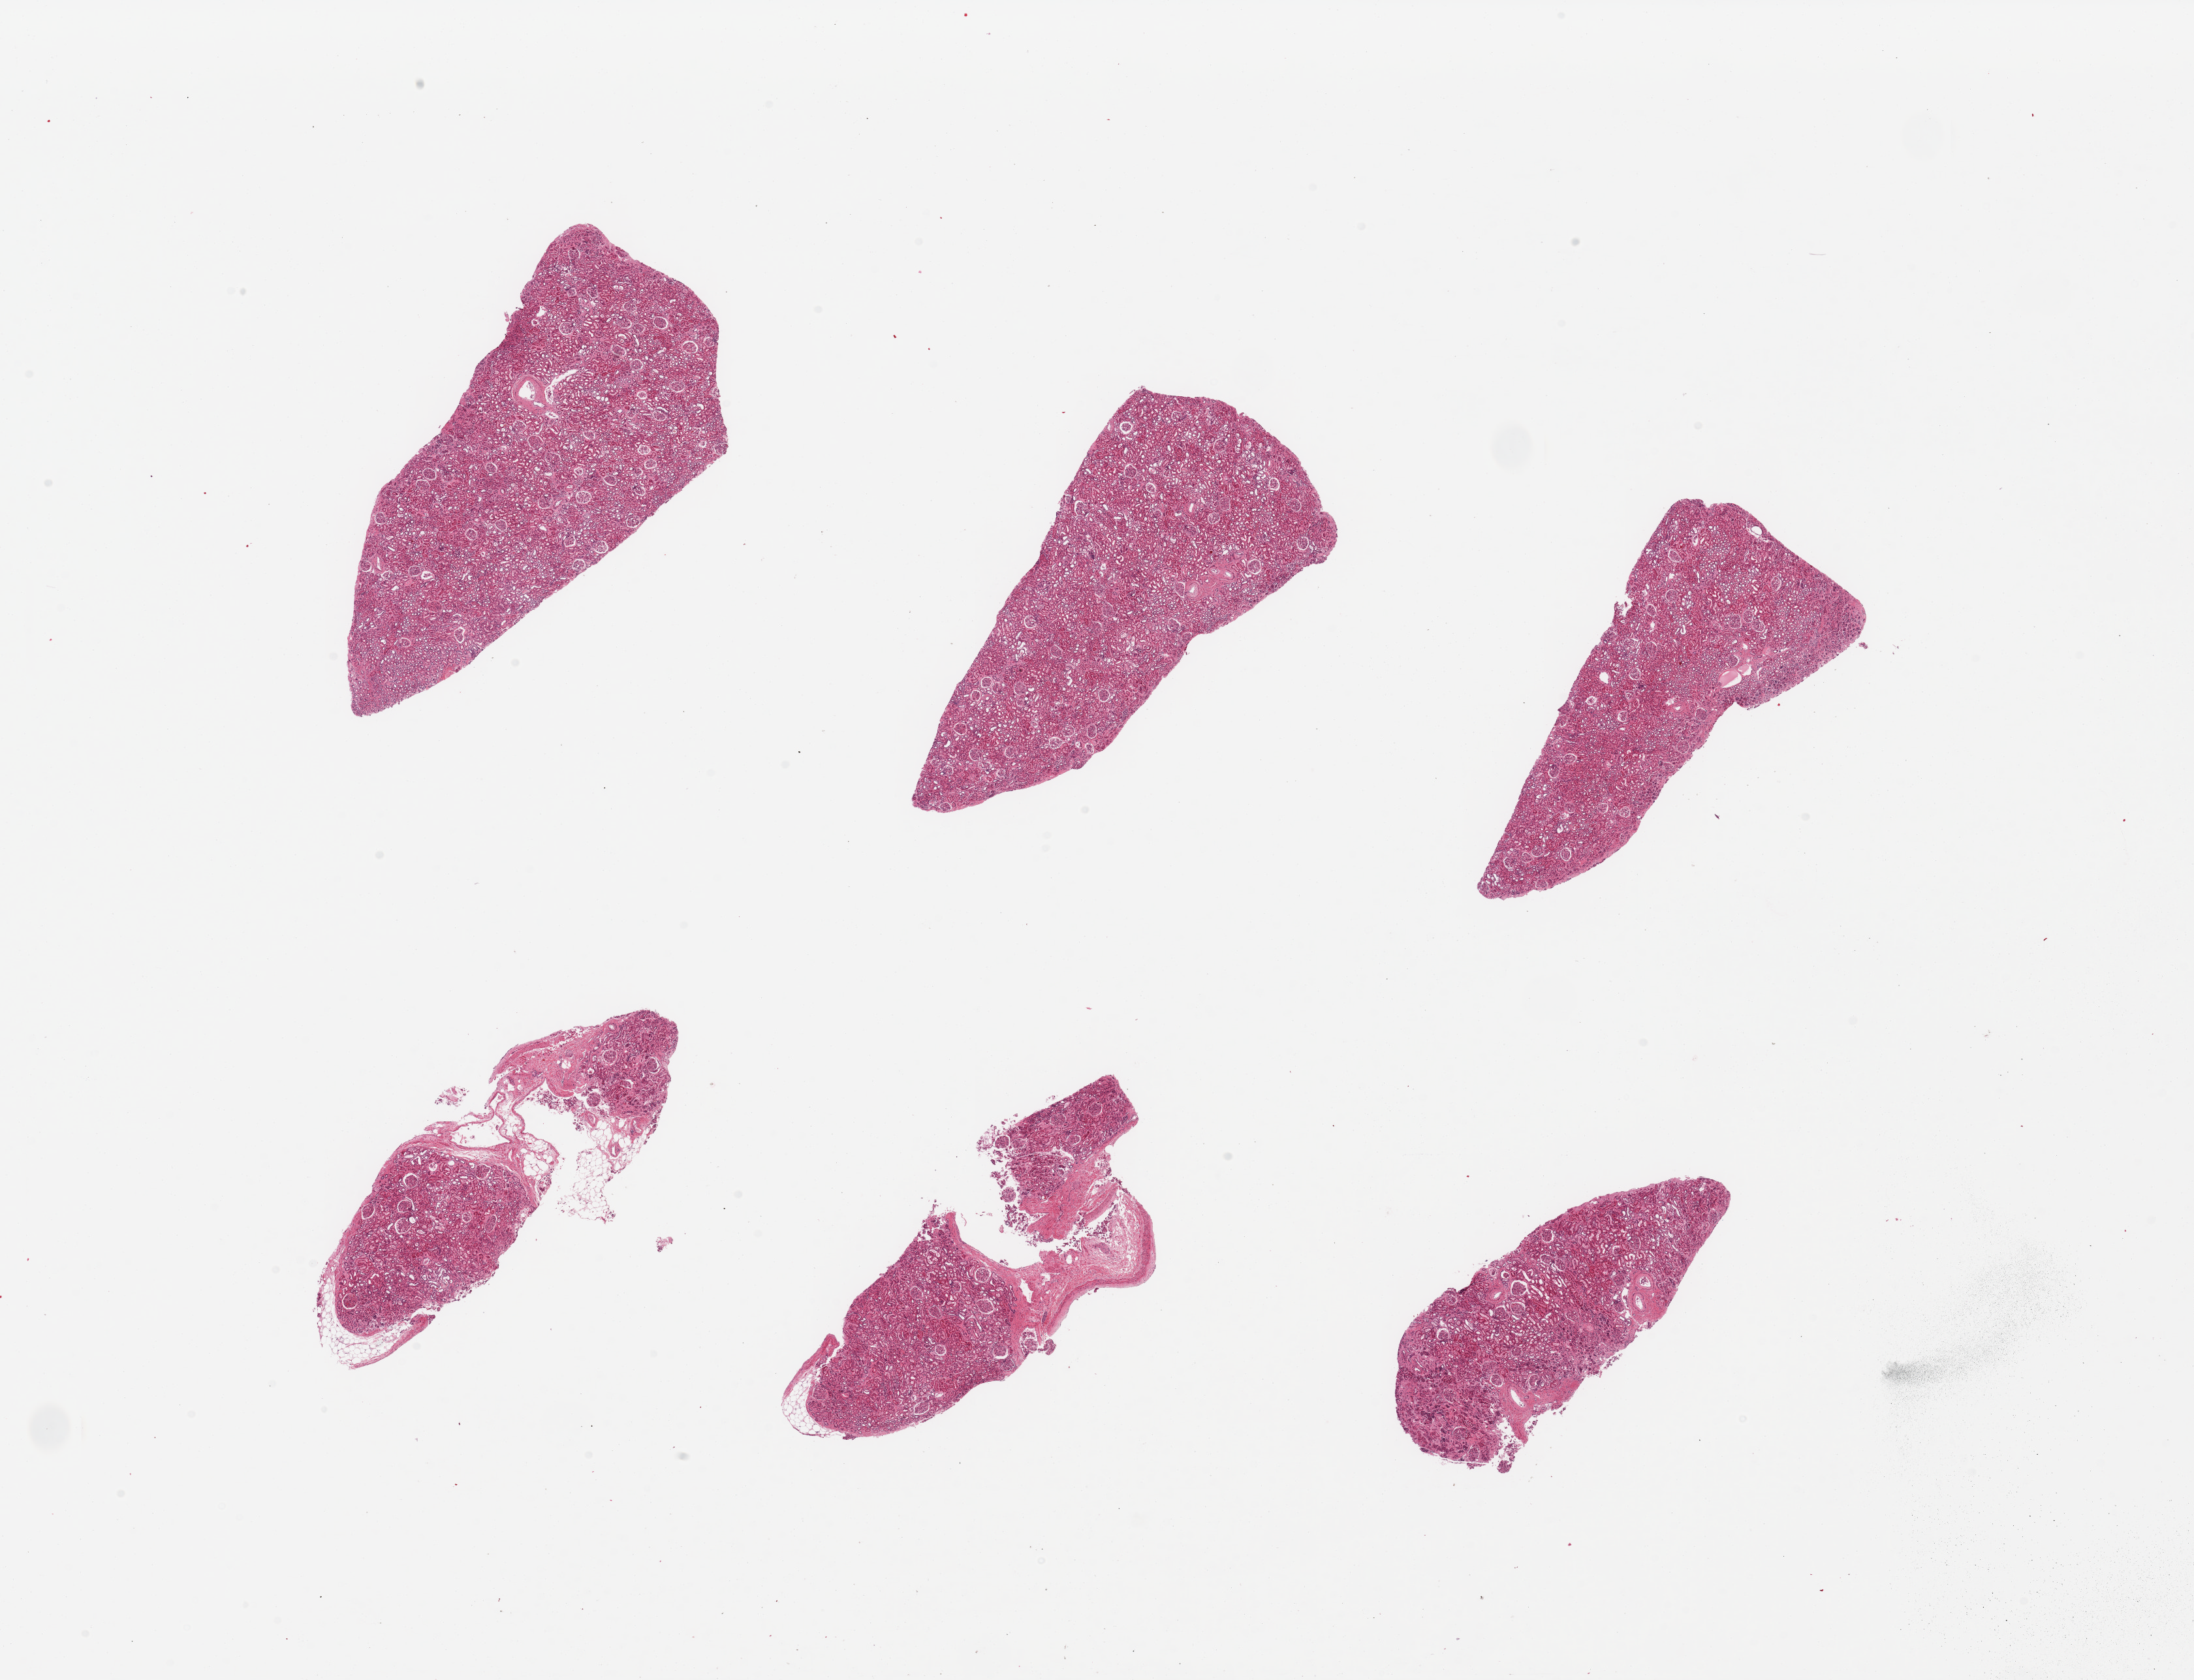
Whole-slide image, H&E stain, shown as a low-resolution overview of the whole scanned area (about 26.6 x 20.4 mm); PAXgene-fixed paraffin-embedded (PFPE) section; sampled site (target tissue): renal cortex; donor tissue sample. Donor sex: male.
* pathologist's review note for this sample: 6 pieces; glomeruli in all sections, some vascular thickening